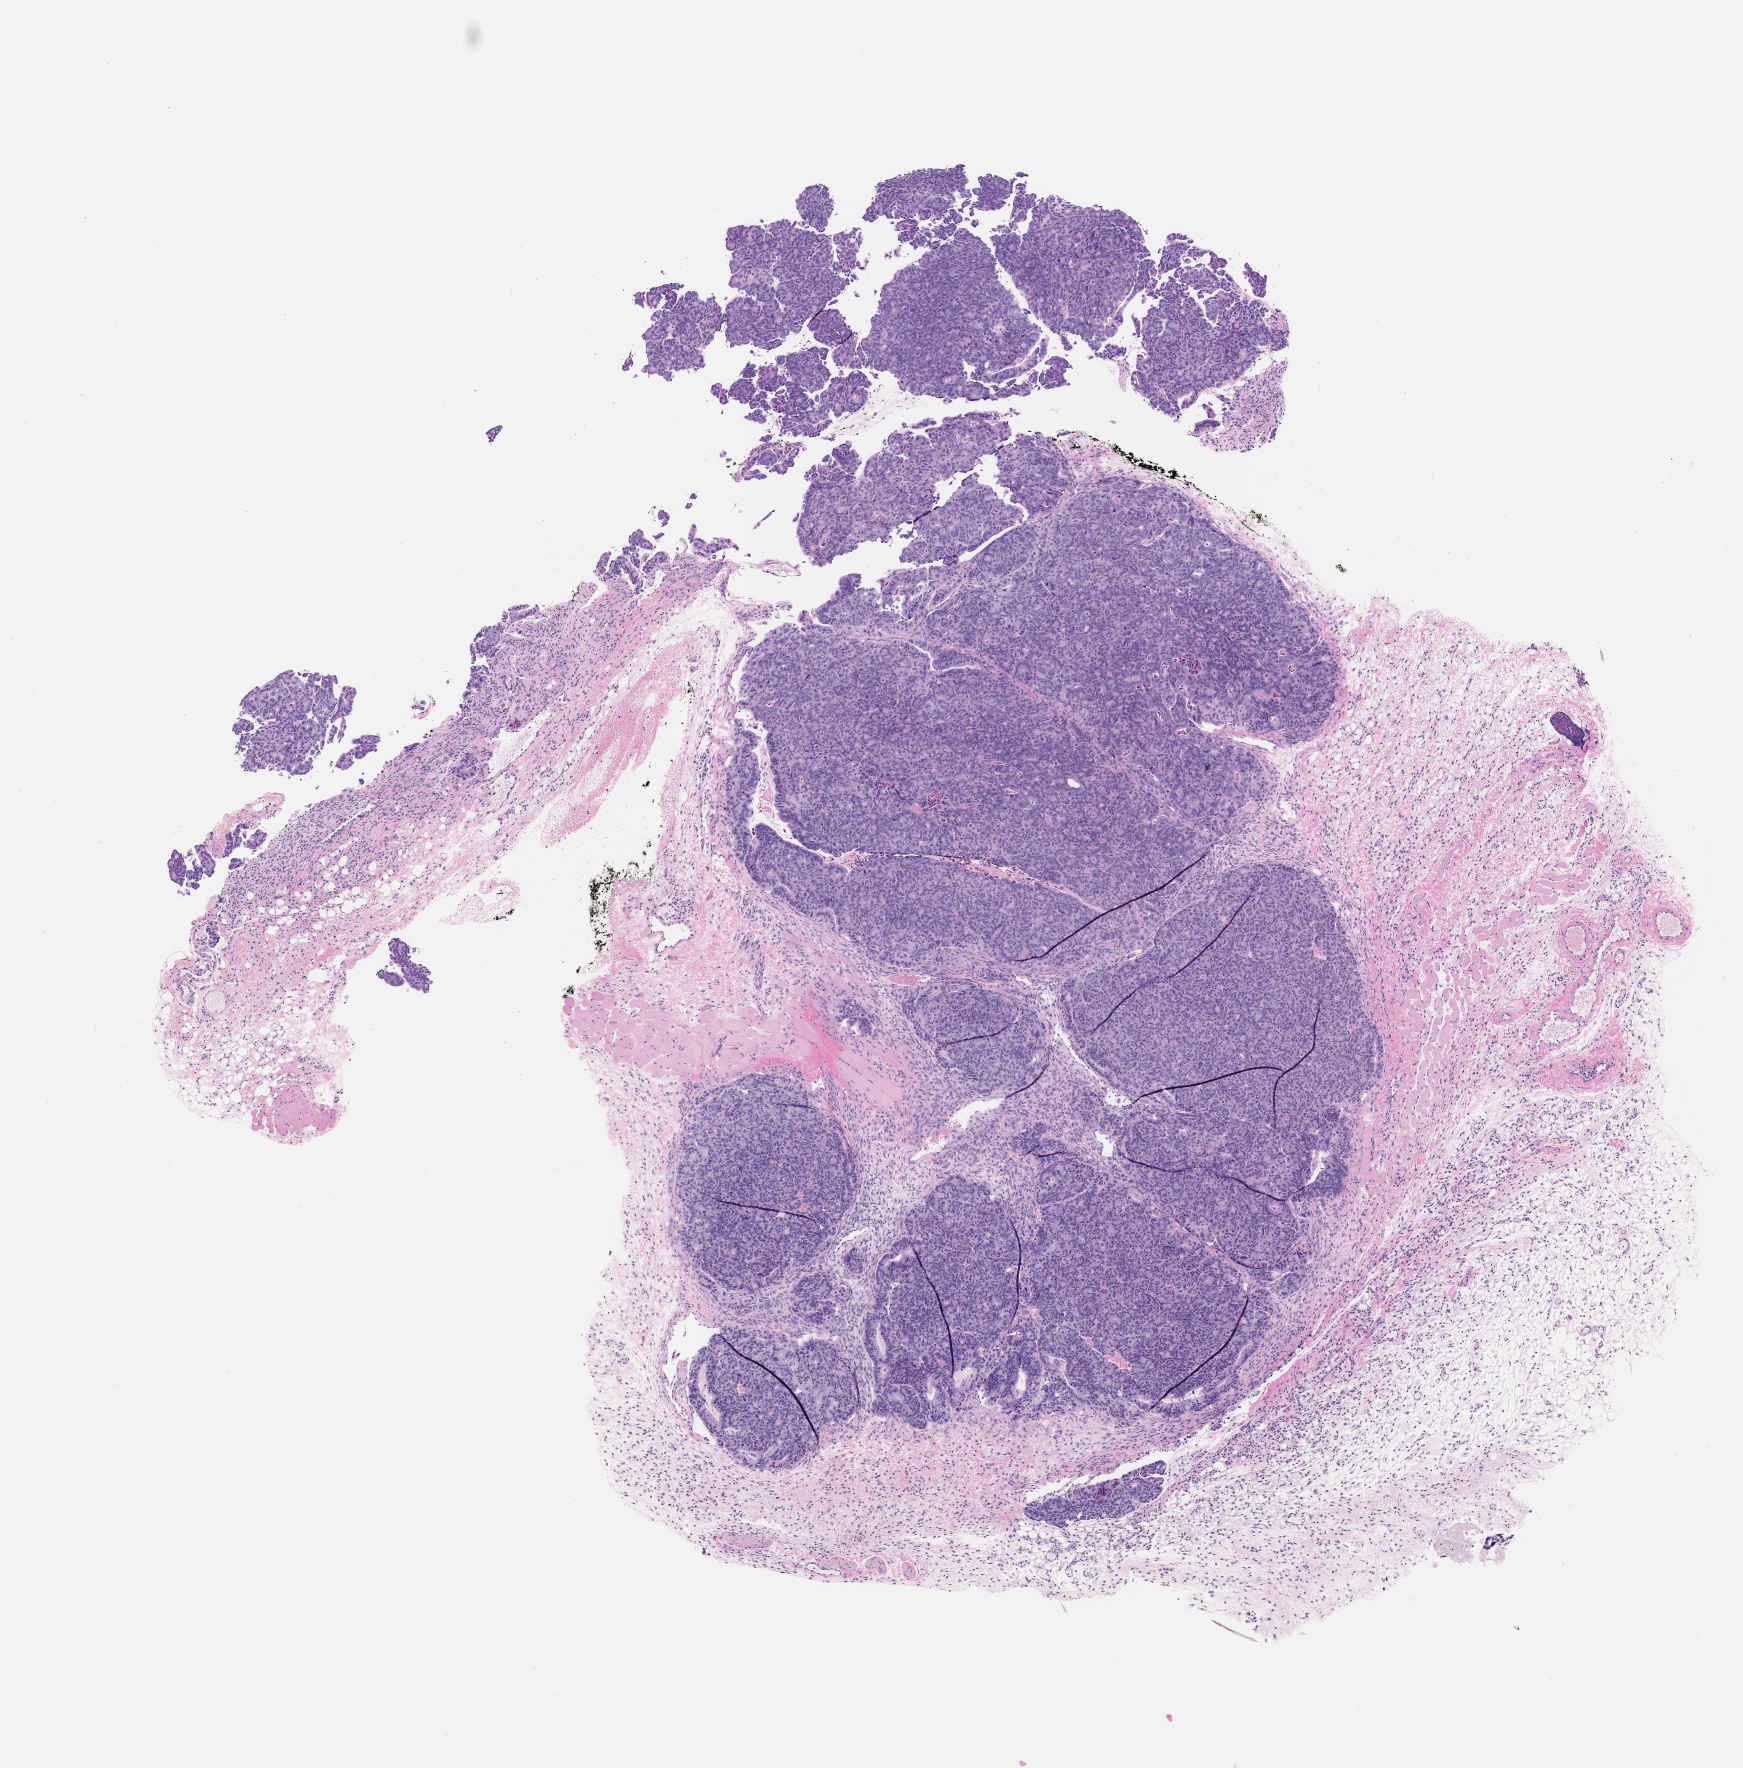
Whole-slide image, hematoxylin and eosin (H&E): patient-derived xenograft (human tumor grown in a mouse), passage 1 — low-resolution overview of the scanned area, about 7.0 x 7.1 mm. Formalin-fixed, paraffin-embedded (FFPE) tissue. Tumor site category: colon.
- originating patient diagnosis: Colon Adenocarcinoma